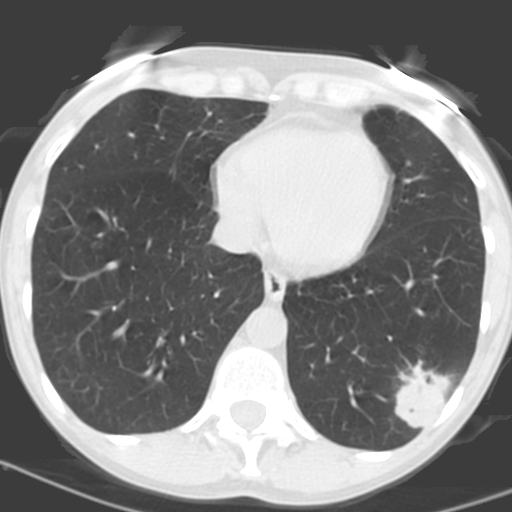
Low-dose screening chest CT, axial slice, first (baseline) screen, lung window (W 1500 / L -600 HU), 3.2 mm slice thickness, standard (soft-tissue) reconstruction kernel (C), 120 kVp, slice 106 of 156 in the series. Female, age 56 years at enrolment.
• Expert-annotated lung lesion, bounding box <383,360,461,430> (left, top, right, bottom; pixels).
• The exam's reader record, not a measurement of the box and not confirmed to be the same lesion: non-calcified nodule or mass ≥4 mm, left lower lobe, 31 × 23 mm, poorly defined margins, soft tissue attenuation, pre-existing on the prior screen: no.
• Official screen result: positive, change unspecified: nodule(s) >= 4 mm or enlarging nodule(s), mass(es), or other non-specific abnormalities suspicious for lung cancer.
• Later outcome: lung cancer diagnosed 27 days after this screen — squamous cell carcinoma, NOS, left lower lobe, poorly differentiated (G3), stage IB (AJCC 6th edition), 35 mm at pathology.